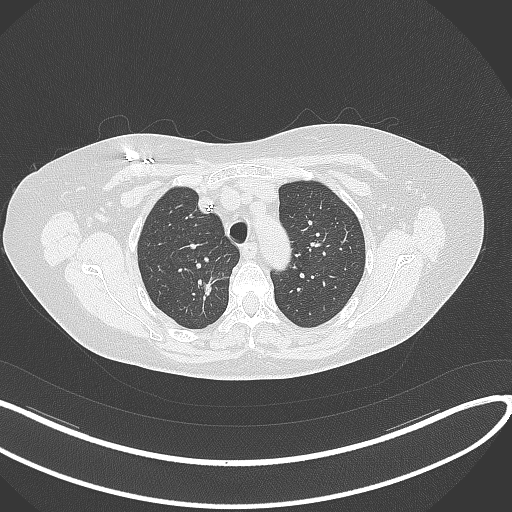
Chest CT, one axial slice. Slice 260 of 316 in the series (ordered by position). Reconstruction kernel B70f. Lung window (W 1500 / L -600 HU). 1 mm slice thickness. 512 × 512 image matrix. Patient: female, 72 years. Case-level facts recorded for this patient, not image findings: clinical TNM (as recorded): T1c N0 M0.
Annotated regions visible in this slice (rectangle marked by the reading radiologist):
- lung tumour (recorded histology: adenocarcinoma): bounding box <193,268,223,311> (left, top, right, bottom; pixels)